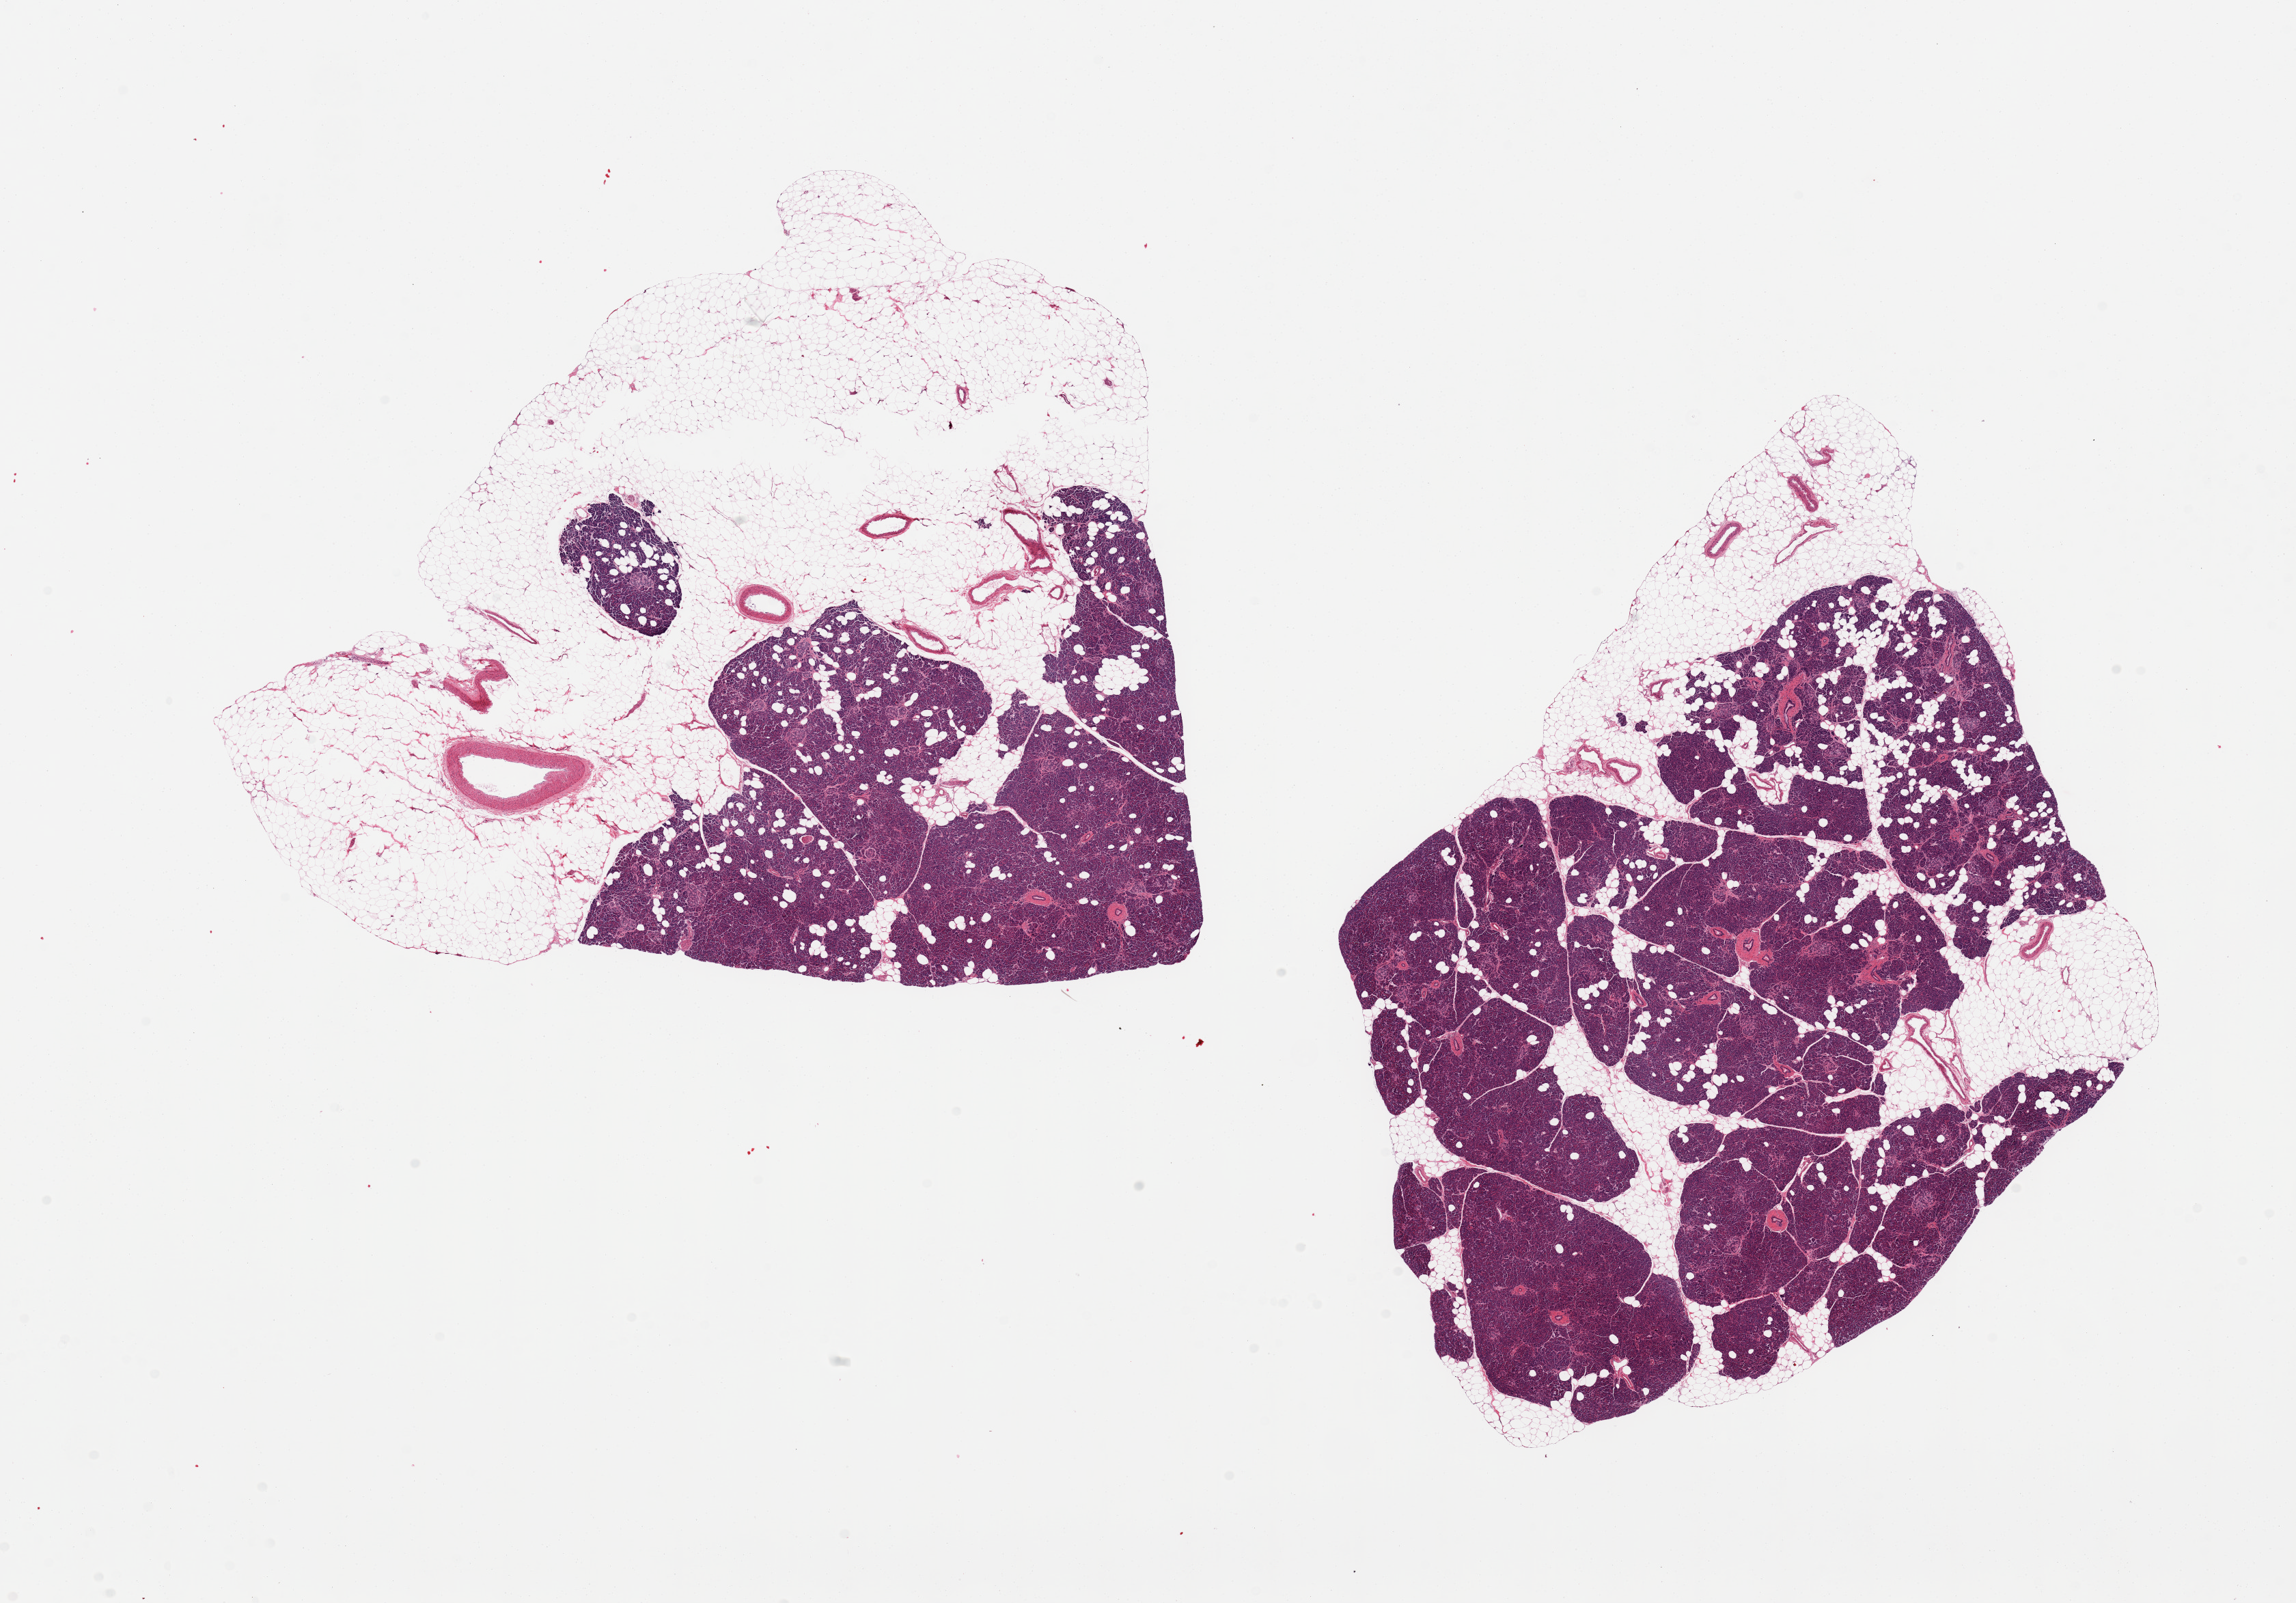
Digitized hematoxylin and eosin (H&E)-stained section — shown as a low-resolution overview of the whole scanned area (about 26.6 x 18.6 mm), PAXgene-fixed paraffin-embedded (PFPE) section, section of pancreas (target tissue), tissue donor sample. Donor: male.
Pathologist's review note for this sample: 2 pieces, ~40% adherent or interstitial fat; Islets well represented/preserved.